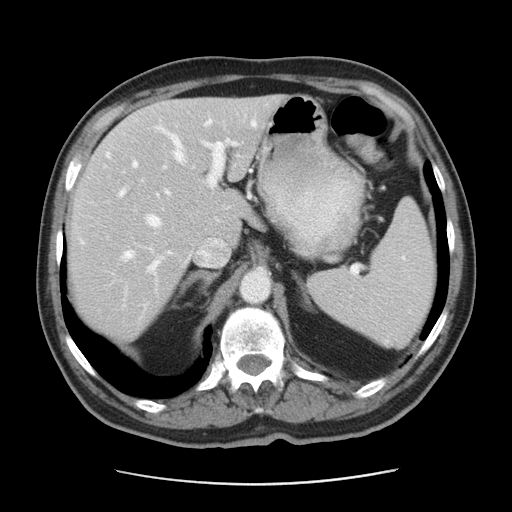
Contrast-enhanced abdominal CT, one axial slice; reconstruction kernel STANDARD; 120 kVp; intravenous contrast given; soft-tissue window (W 400 / L 40 HU); 5 mm slice thickness; 512 × 512 image matrix, field of view 370 × 370 mm. Male patient, age 73 years. From the clinical record (not read from this slice): diagnosis: colorectal cancer liver metastases, imaged before liver resection; multiple liver metastases: yes; largest metastasis: 0.5 cm; disease in both lobes: no.
Outlined on this slice (manually delineated by an expert):
- hepatic veins: bounding box <120,118,256,320> (left, top, right, bottom; pixels)
- liver: <68,96,277,338>
- planned liver remnant (the part of the liver to remain after resection): <114,96,277,243>
- portal vein (with intrahepatic branches): <121,139,231,275>